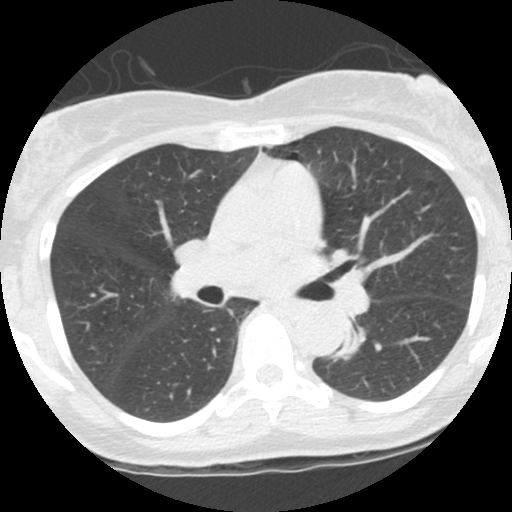
Low-dose screening chest CT, one axial slice; slice 63 of 115 in the series (ordered by position); reconstruction kernel STANDARD; 120 kVp; lung window (W 1500 / L -600 HU); 2.5 mm slice thickness; 512 × 512 image matrix, field of view 290 × 290 mm.
Outlined on this slice (manually delineated by an expert):
- lesion 1 (tumor, lower lobe of left lung): box from (x=337, y=333) to (x=362, y=357) px